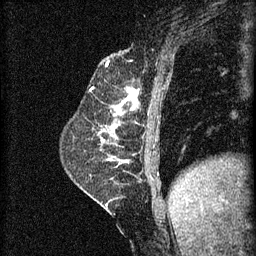
Breast MRI (dynamic contrast-enhanced), one sagittal slice; position 20 of 60 along the scan axis; 3 images stored at this slice position (order not interpretable as contrast timing); 1.5 T; TE 4.2 ms, TR 8.2 ms; 256 × 256 image matrix. Female patient, age 59 years.
Structures marked on this image (semi-automatically segmented with operator editing):
- analysis volume of interest (the breast-tissue region the enhancement analysis was run in; not a lesion): bounding box (x1, y1, x2, y2) in pixels: (100, 92, 137, 135)
- tumour enhancement mask (voxels above the 70 % enhancement threshold inside the analysis volume of interest): (120, 92, 137, 107)